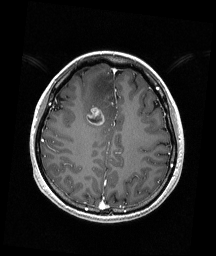
Brain MRI from a brain-tumour surgery series, one axial slice; slice 62 of 192 in the series (ordered by position); T1-weighted post-contrast; 1 mm slice thickness; 216 × 256 image matrix, field of view 211 × 250 mm. Case-level facts recorded for this patient, not image findings: histopathology: Astrocytoma; WHO grade: 4; IDH mutation: yes.
Annotated regions visible in this slice (outlined manually by an expert reader):
- tumour: bounding box <87,106,105,126> (left, top, right, bottom; pixels)